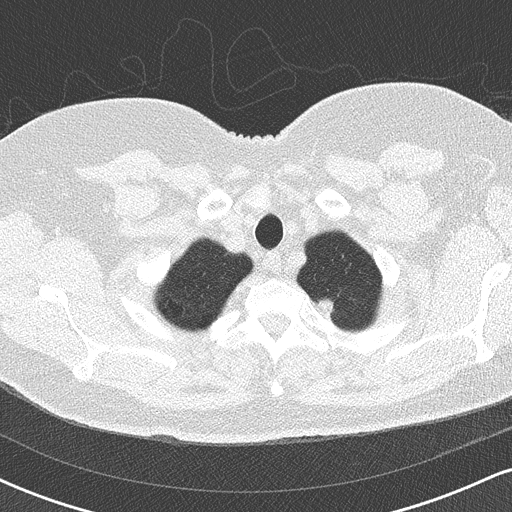
Chest CT (low-dose screening protocol), one axial image. Third screening round (two years after baseline). Lung window (W 1500 / L -600 HU). 2 mm slice thickness. Lung (sharp) reconstruction kernel (B50f). 120 kVp. Slice 18 of 170 in the series. Female, age 60 years at enrolment. Former smoker at enrolment.
Expert reader's lesion annotation, bounding box <299,285,348,328> (left, top, right, bottom; pixels). Screening reader's record for this exam (one nodule recorded; not confirmed to be the boxed lesion): non-calcified nodule or mass ≥4 mm, left upper lobe, 10 × 10 mm, soft tissue attenuation, pre-existing on the prior screen: yes. Later outcome: lung cancer diagnosed 94 days after this screen — non-small cell carcinoma, left upper lobe, poorly differentiated (G3), stage IB (AJCC 6th edition), 16 mm at pathology.